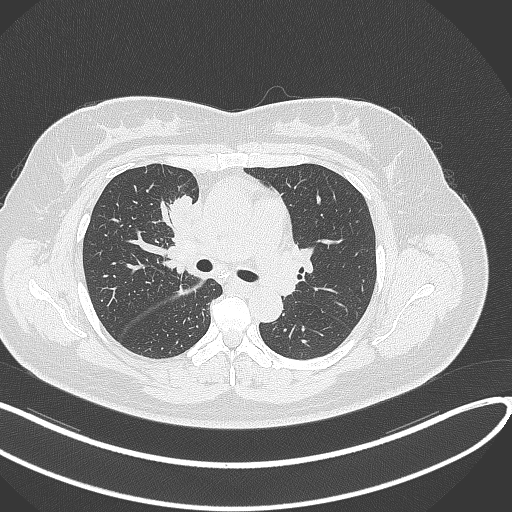
Chest CT, one axial slice. Position 170 of 303 along the scan axis. 120 kVp. Lung window (W 1500 / L -600 HU). 1 mm slice thickness. 512 × 512 image matrix, field of view 400 × 400 mm. Female patient, age 46 years. Case-level facts recorded for this patient, not image findings: clinical TNM (as recorded): T2a N1 M0.
Outlined on this slice (bounding box drawn by a radiologist):
- lung tumour (recorded histology: adenocarcinoma): bounding box [x1, y1, x2, y2] px = [164, 192, 198, 233]